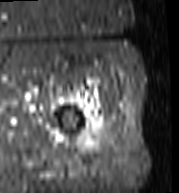
MRI of an extremity soft-tissue mass, one axial slice. Slice 92 of 103 in the series (ordered by position). STIR. MR volume resampled by the dataset authors to the PET/CT grid (not the native acquisition matrix). 3.27 mm slice thickness. 179 × 193 image matrix, field of view 175 × 188 mm. Female patient. From the clinical record (not read from this slice): histological type: undifferentiated – high grade; grade: high; site of the primary tumour: left thigh.
Structures marked on this image (expert contour drawn on MRI and transferred to this co-registered scan by the dataset authors):
- gross tumour volume including surrounding oedema: bounding box (x1, y1, x2, y2) in pixels: (72, 99, 110, 156)
- gross tumour volume (mass): (82, 128, 103, 143)